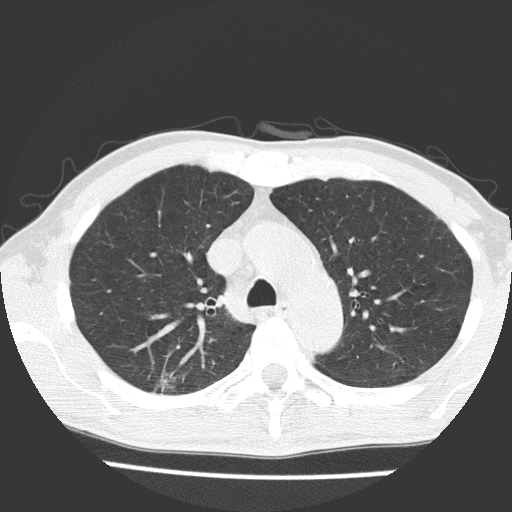
Chest CT (low-dose screening protocol), one axial image; first (baseline) screen; lung window (W 1500 / L -600 HU); 2 mm slice thickness; lung (sharp) reconstruction kernel (FC51); 120 kVp; slice 45 of 160 in the series. Male participant, aged 66 years at enrolment.
- Expert reader's lesion annotation, box from (x=143, y=361) to (x=192, y=409) px.
- The exam's reader record, not a measurement of the box and not confirmed to be the same lesion: non-calcified nodule or mass ≥4 mm, right upper lobe, 15 × 10 mm, spiculated (stellate) margins, soft tissue attenuation.
- Official screen result: positive, change unspecified: nodule(s) >= 4 mm or enlarging nodule(s), mass(es), or other non-specific abnormalities suspicious for lung cancer.